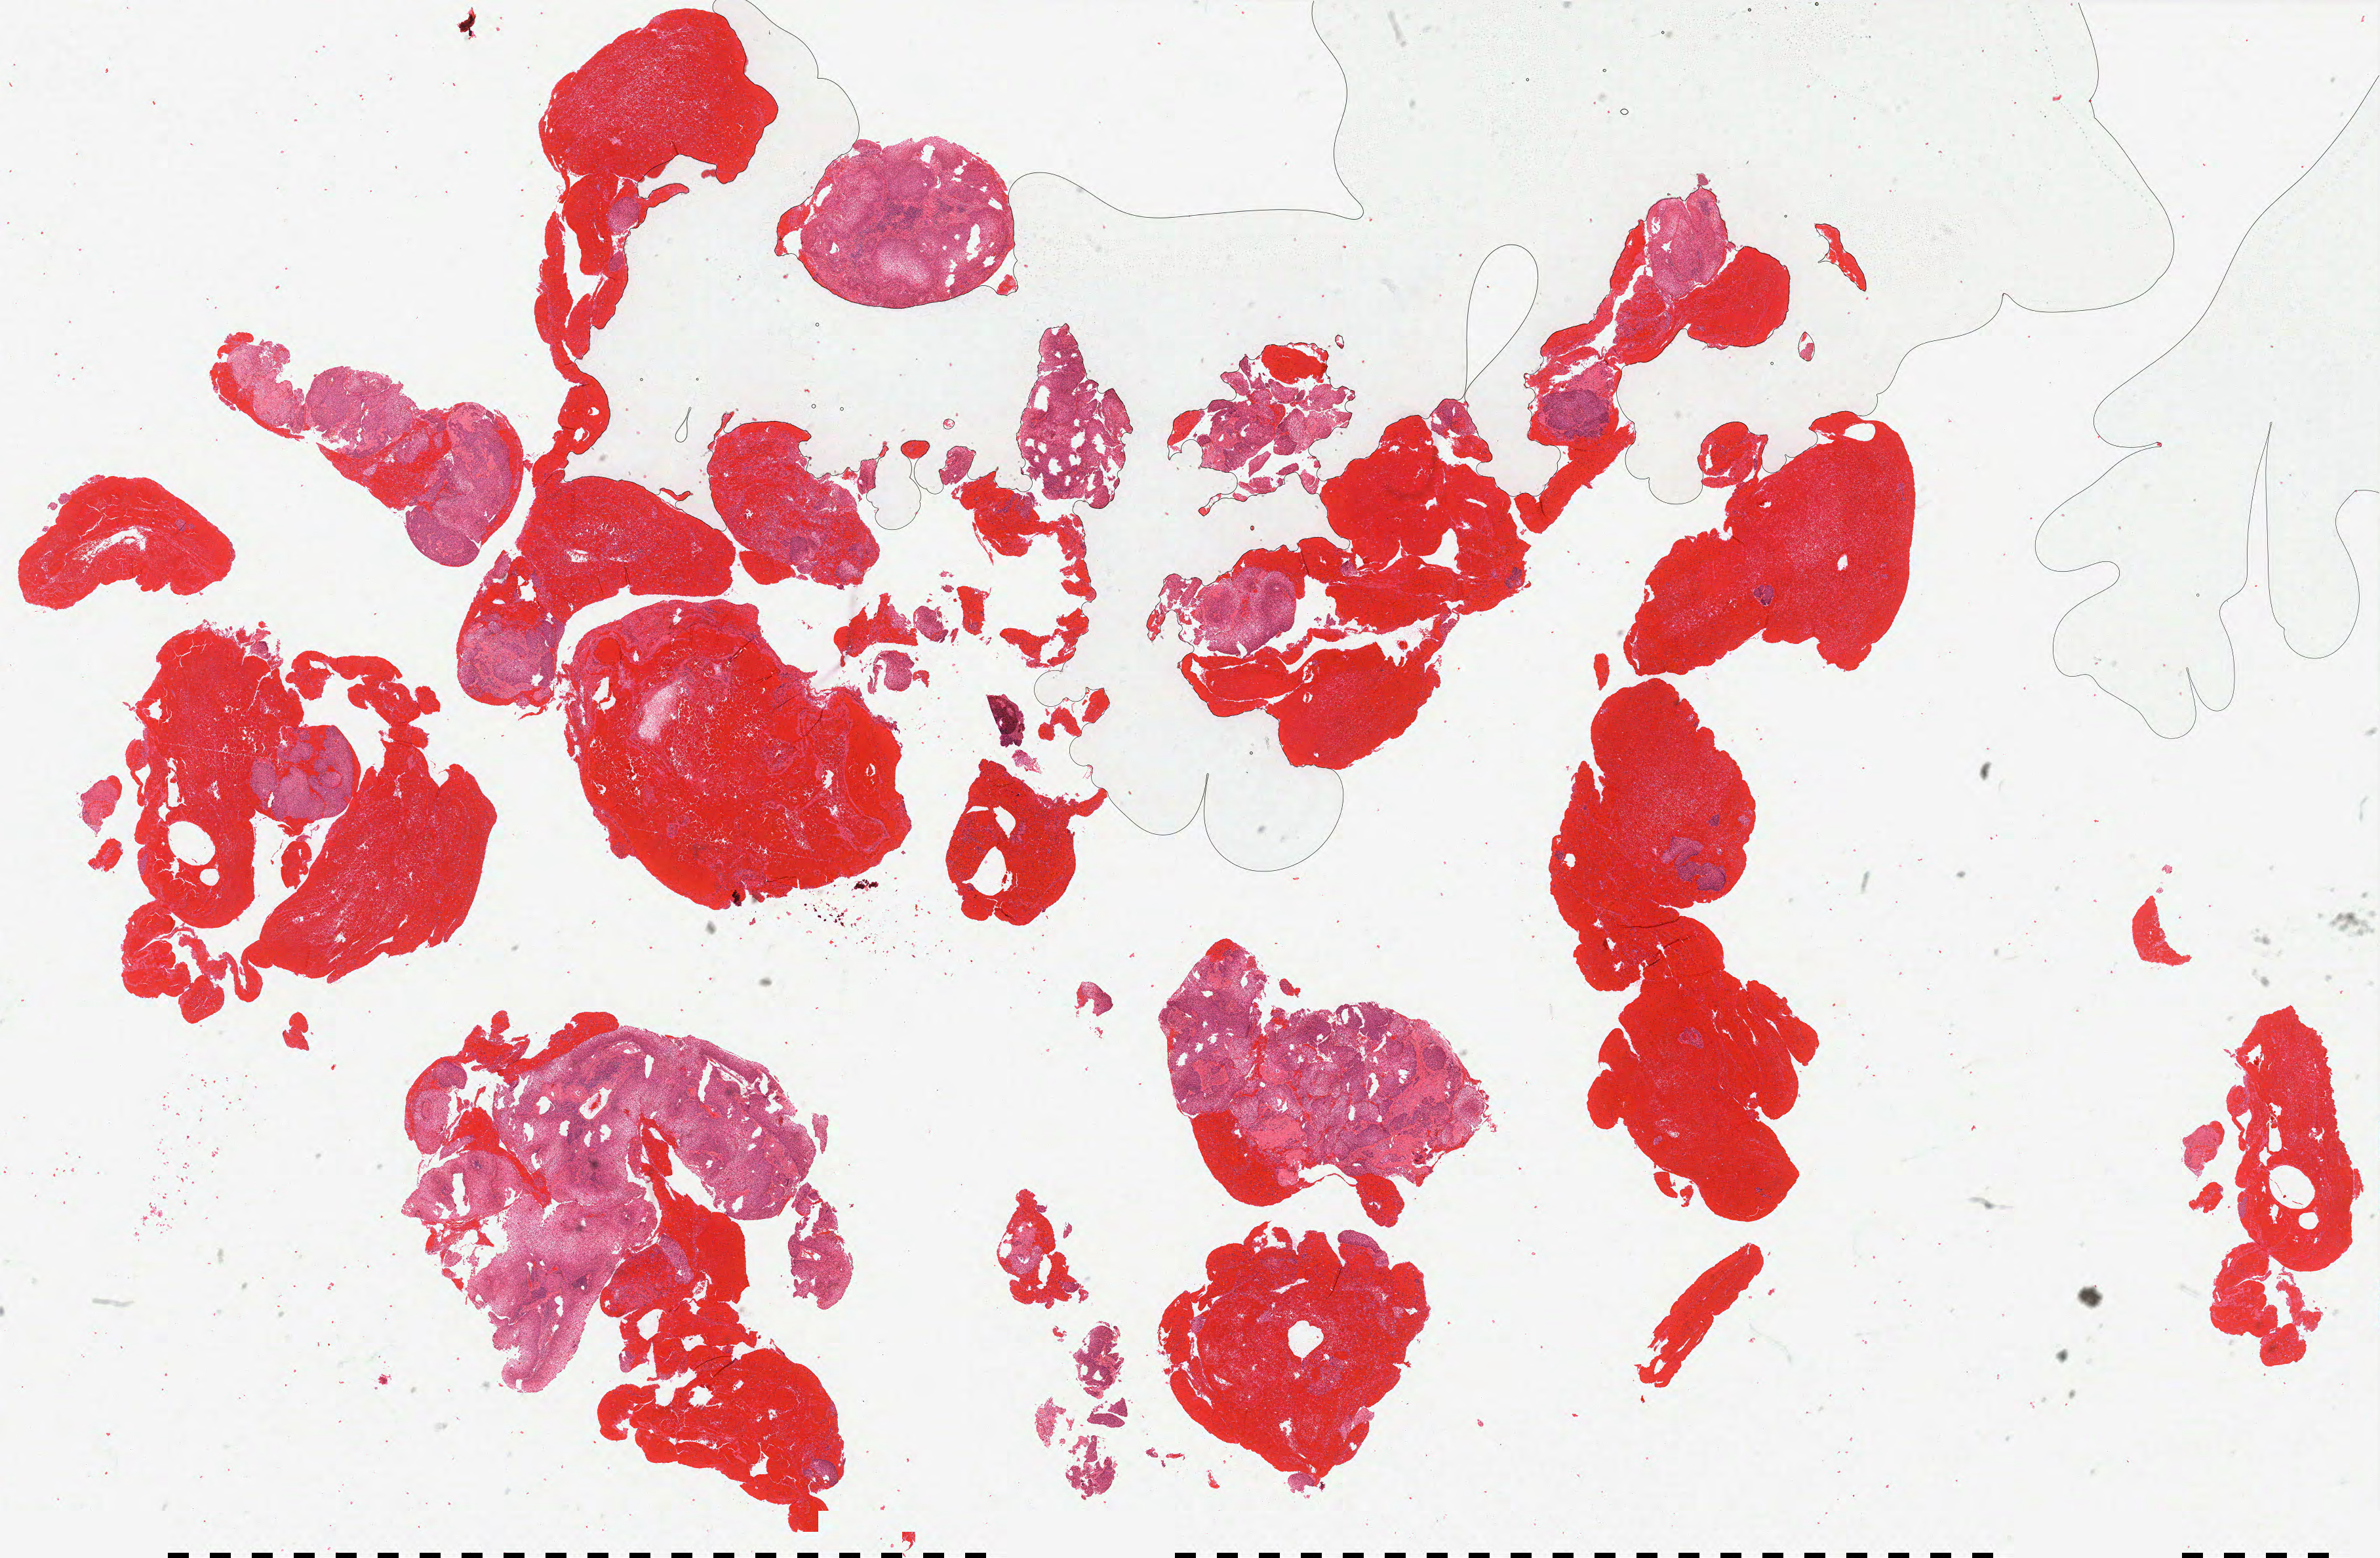
H&E whole-slide image — low-resolution overview of the scanned area, about 29.1 x 19.0 mm (acquisition: 40x scan), FFPE section, sample: primary tumour, cervix. Patient: female, age at initial diagnosis 48 years. Histologic grade: G2 (moderately differentiated).
Diagnosis: Squamous cell carcinoma, NOS (cervix uteri). FIGO stage: IIIB.